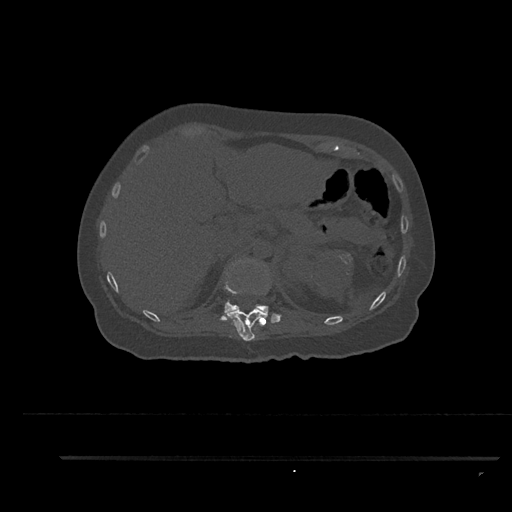
CT including the spine, one axial slice; slice 292 of 797 in the series (ordered by position); reconstruction kernel Br40s/3; 120 kVp; bone window (W 1800 / L 400 HU); 0.5 mm slice thickness; 512 × 512 image matrix, field of view 408 × 408 mm. Female patient, age 44 years. Case-level facts recorded for this patient, not image findings: primary cancer: renal; vertebrae with lytic lesions (as recorded): L1.
Structures marked on this image (semi-automatically segmented with operator editing):
- T11 vertebra: bounding box <229,293,268,341> (left, top, right, bottom; pixels)
- T12 vertebra: <220,259,282,321>